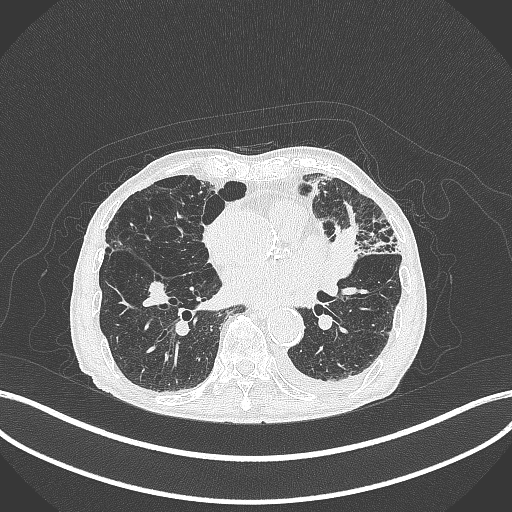
Chest CT, one axial slice; slice 161 of 385 in the series (ordered by position); reconstruction kernel B70f; lung window (W 1500 / L -600 HU); 1 mm slice thickness; 512 × 512 image matrix, field of view 400 × 400 mm. Patient: male, 90 years or older. Case-level facts recorded for this patient, not image findings: clinical TNM (as recorded): T2b N1 M0.
Outlined on this slice (bounding box drawn by a radiologist):
- lung tumour (recorded histology: squamous cell carcinoma): bounding box (x1, y1, x2, y2) in pixels: (329, 218, 365, 282)